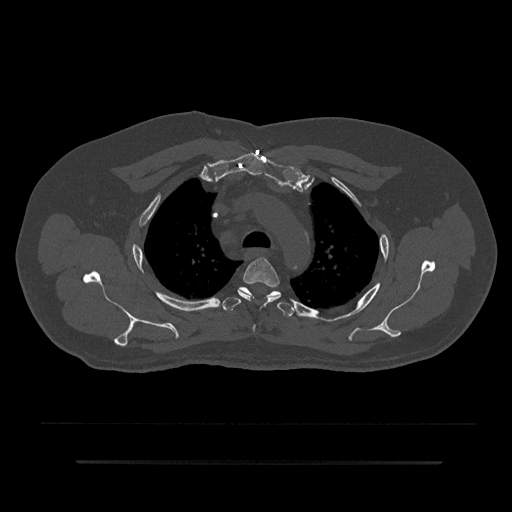
CT including the spine, one axial slice; slice 643 of 797 in the series (ordered by position); reconstruction kernel Br40s/3; bone window (W 1800 / L 400 HU); 0.5 mm slice thickness; 512 × 512 image matrix. Male patient, age 59 years. From the clinical record (not read from this slice): primary cancer: bile ducts; vertebrae with lytic lesions (as recorded): T10.
Outlined on this slice (semi-automatic segmentation, software-assisted and operator-edited):
- T3 vertebra: bounding box [x1, y1, x2, y2] px = [238, 257, 281, 330]
- T4 vertebra: [222, 287, 294, 317]